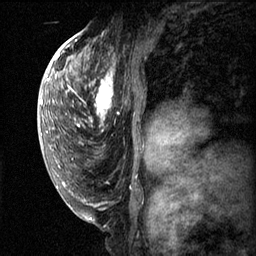
Breast MRI (dynamic contrast-enhanced), one sagittal slice; position 35 of 60 along the scan axis; dynamic contrast-enhanced series, image 2 of 3 at this slice position (ordered by acquisition); 1.5 T; TE 4.2 ms, TR 11.1 ms; 2 mm slice thickness; 256 × 256 image matrix, field of view 180 × 180 mm. Patient: female, 50 years.
Structures marked on this image (semi-automatically segmented with operator editing):
- analysis volume of interest (the breast-tissue region the enhancement analysis was run in; not a lesion): bounding box [x1, y1, x2, y2] px = [82, 56, 160, 143]
- tumour enhancement mask (voxels above the 70 % enhancement threshold inside the analysis volume of interest): [82, 72, 160, 139]